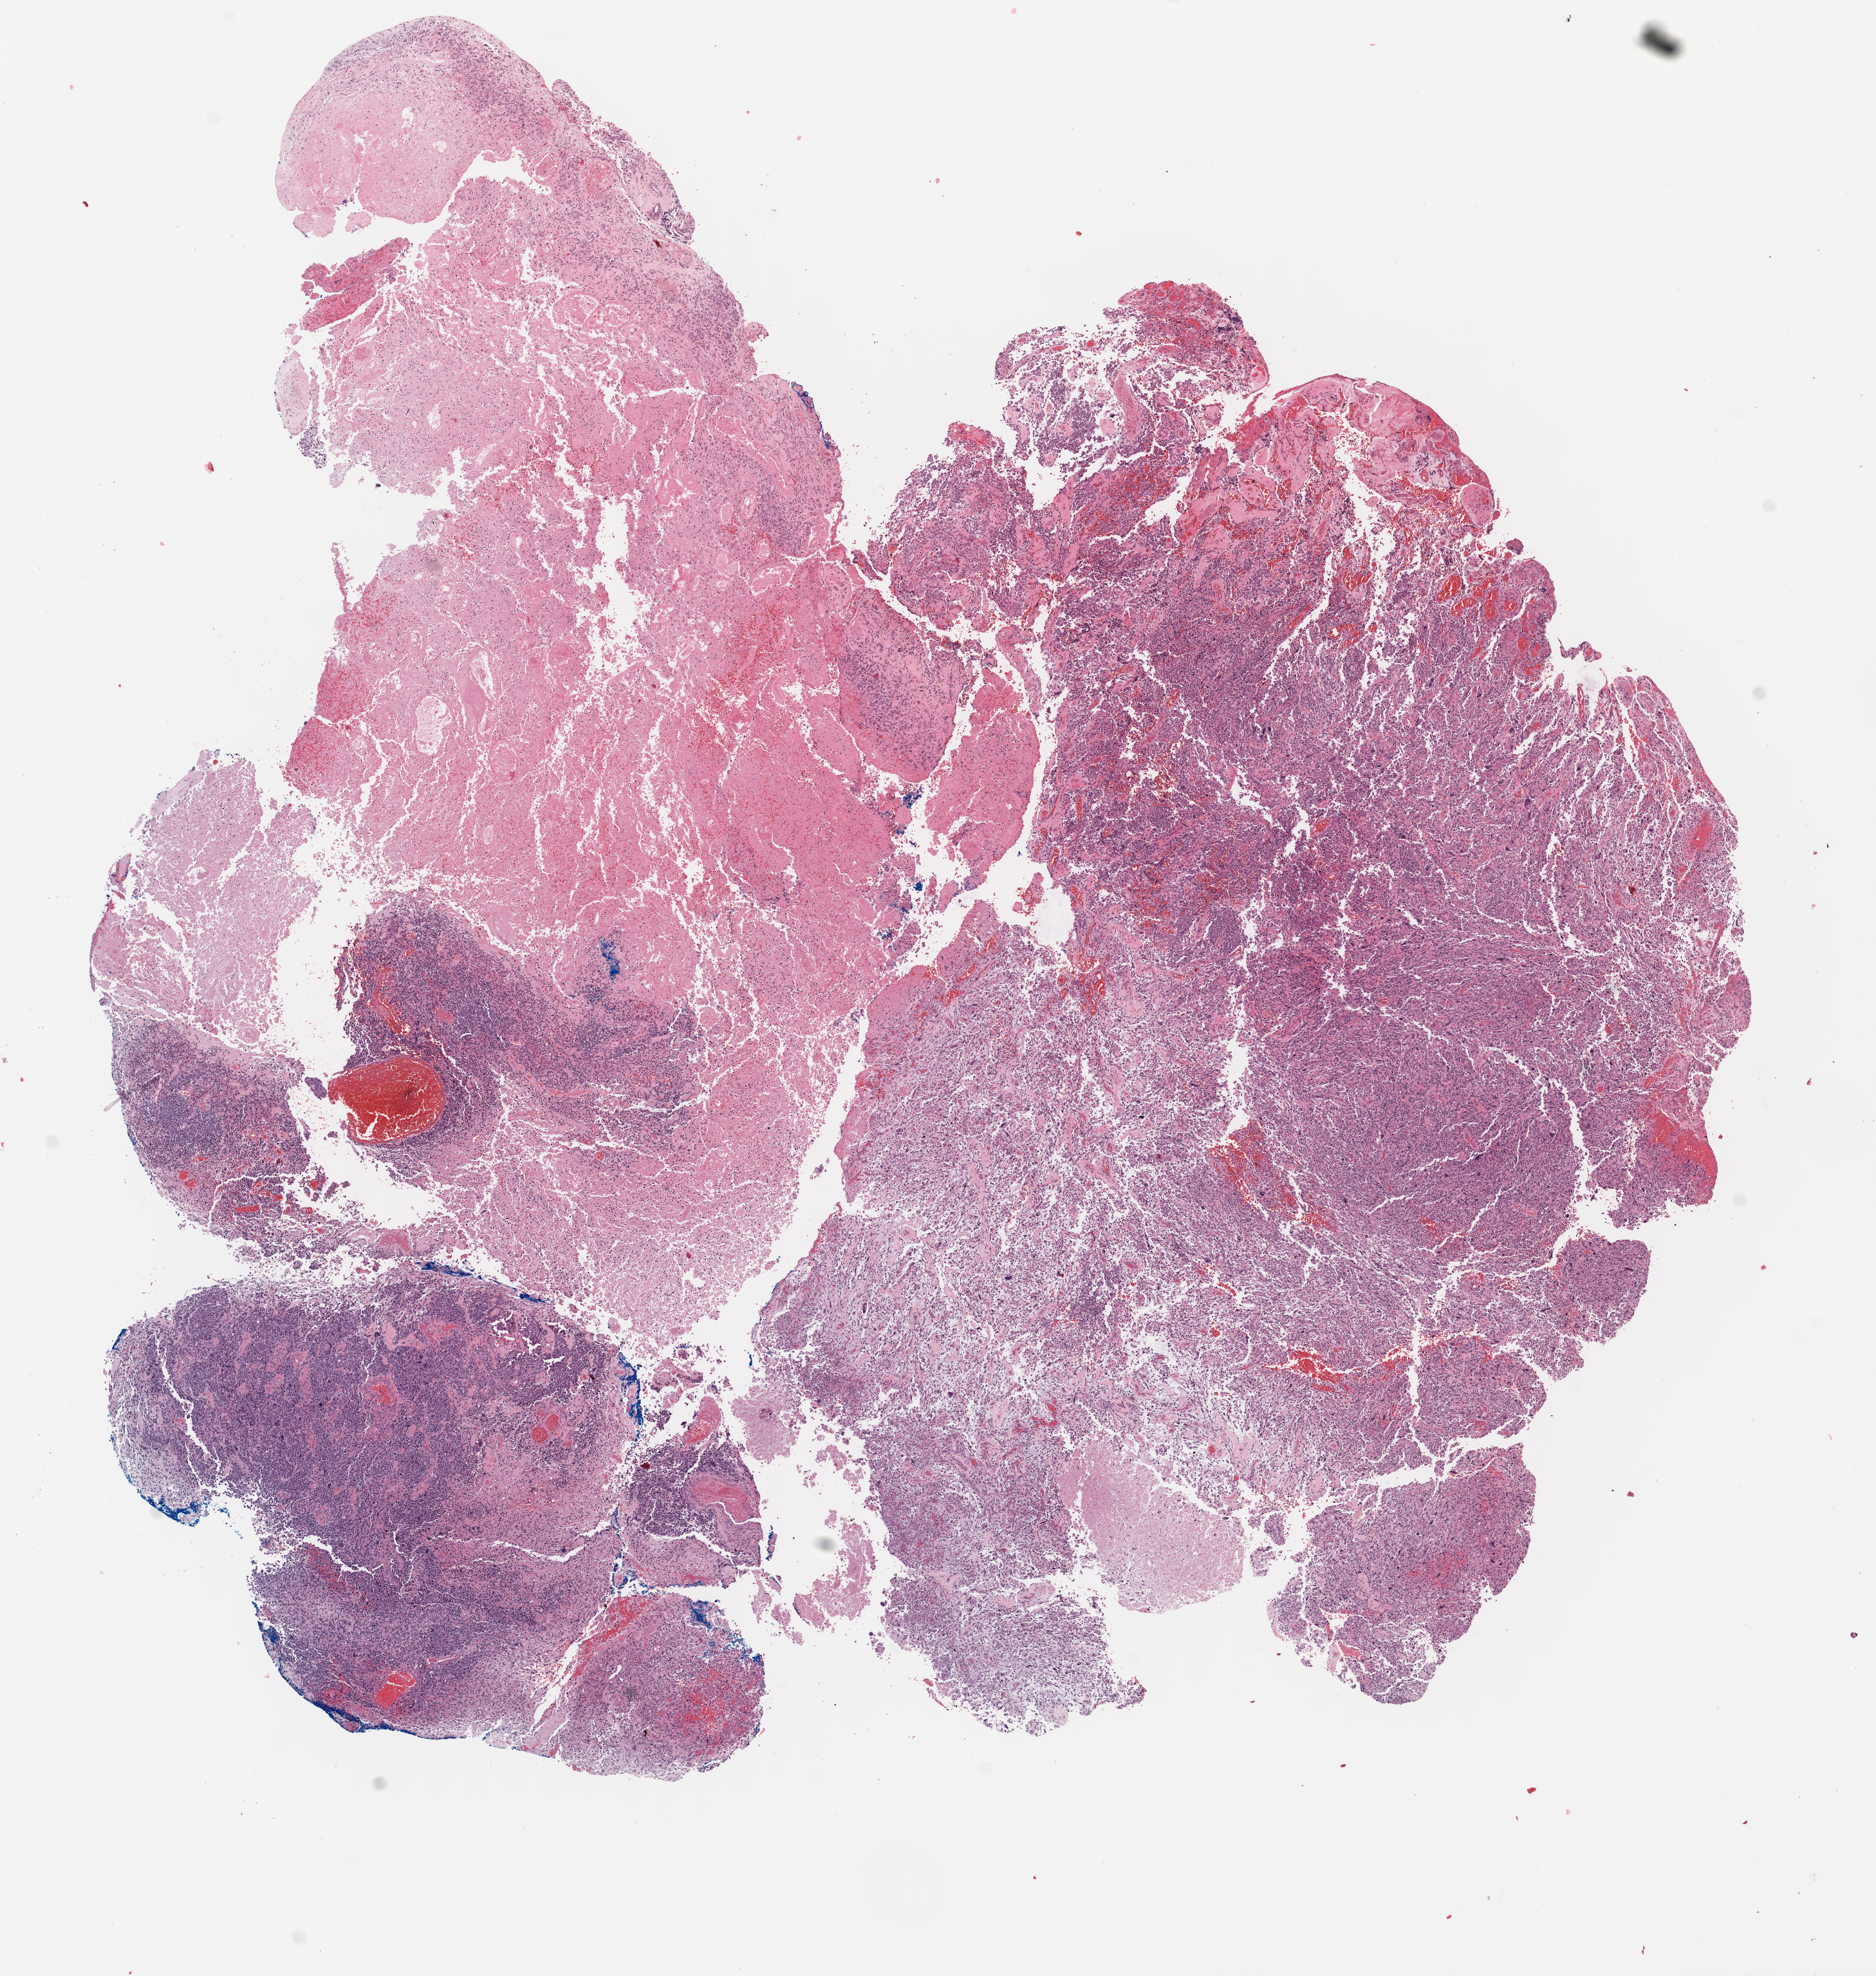
H&E-stained whole-slide image — whole scanned area (about 11.5 x 12.1 mm, slide scanned at 40x) shown as a low-resolution overview, FFPE section, primary tumour sample from the brain. Male patient; age at initial diagnosis 39 years.
* histologic diagnosis: Glioblastoma